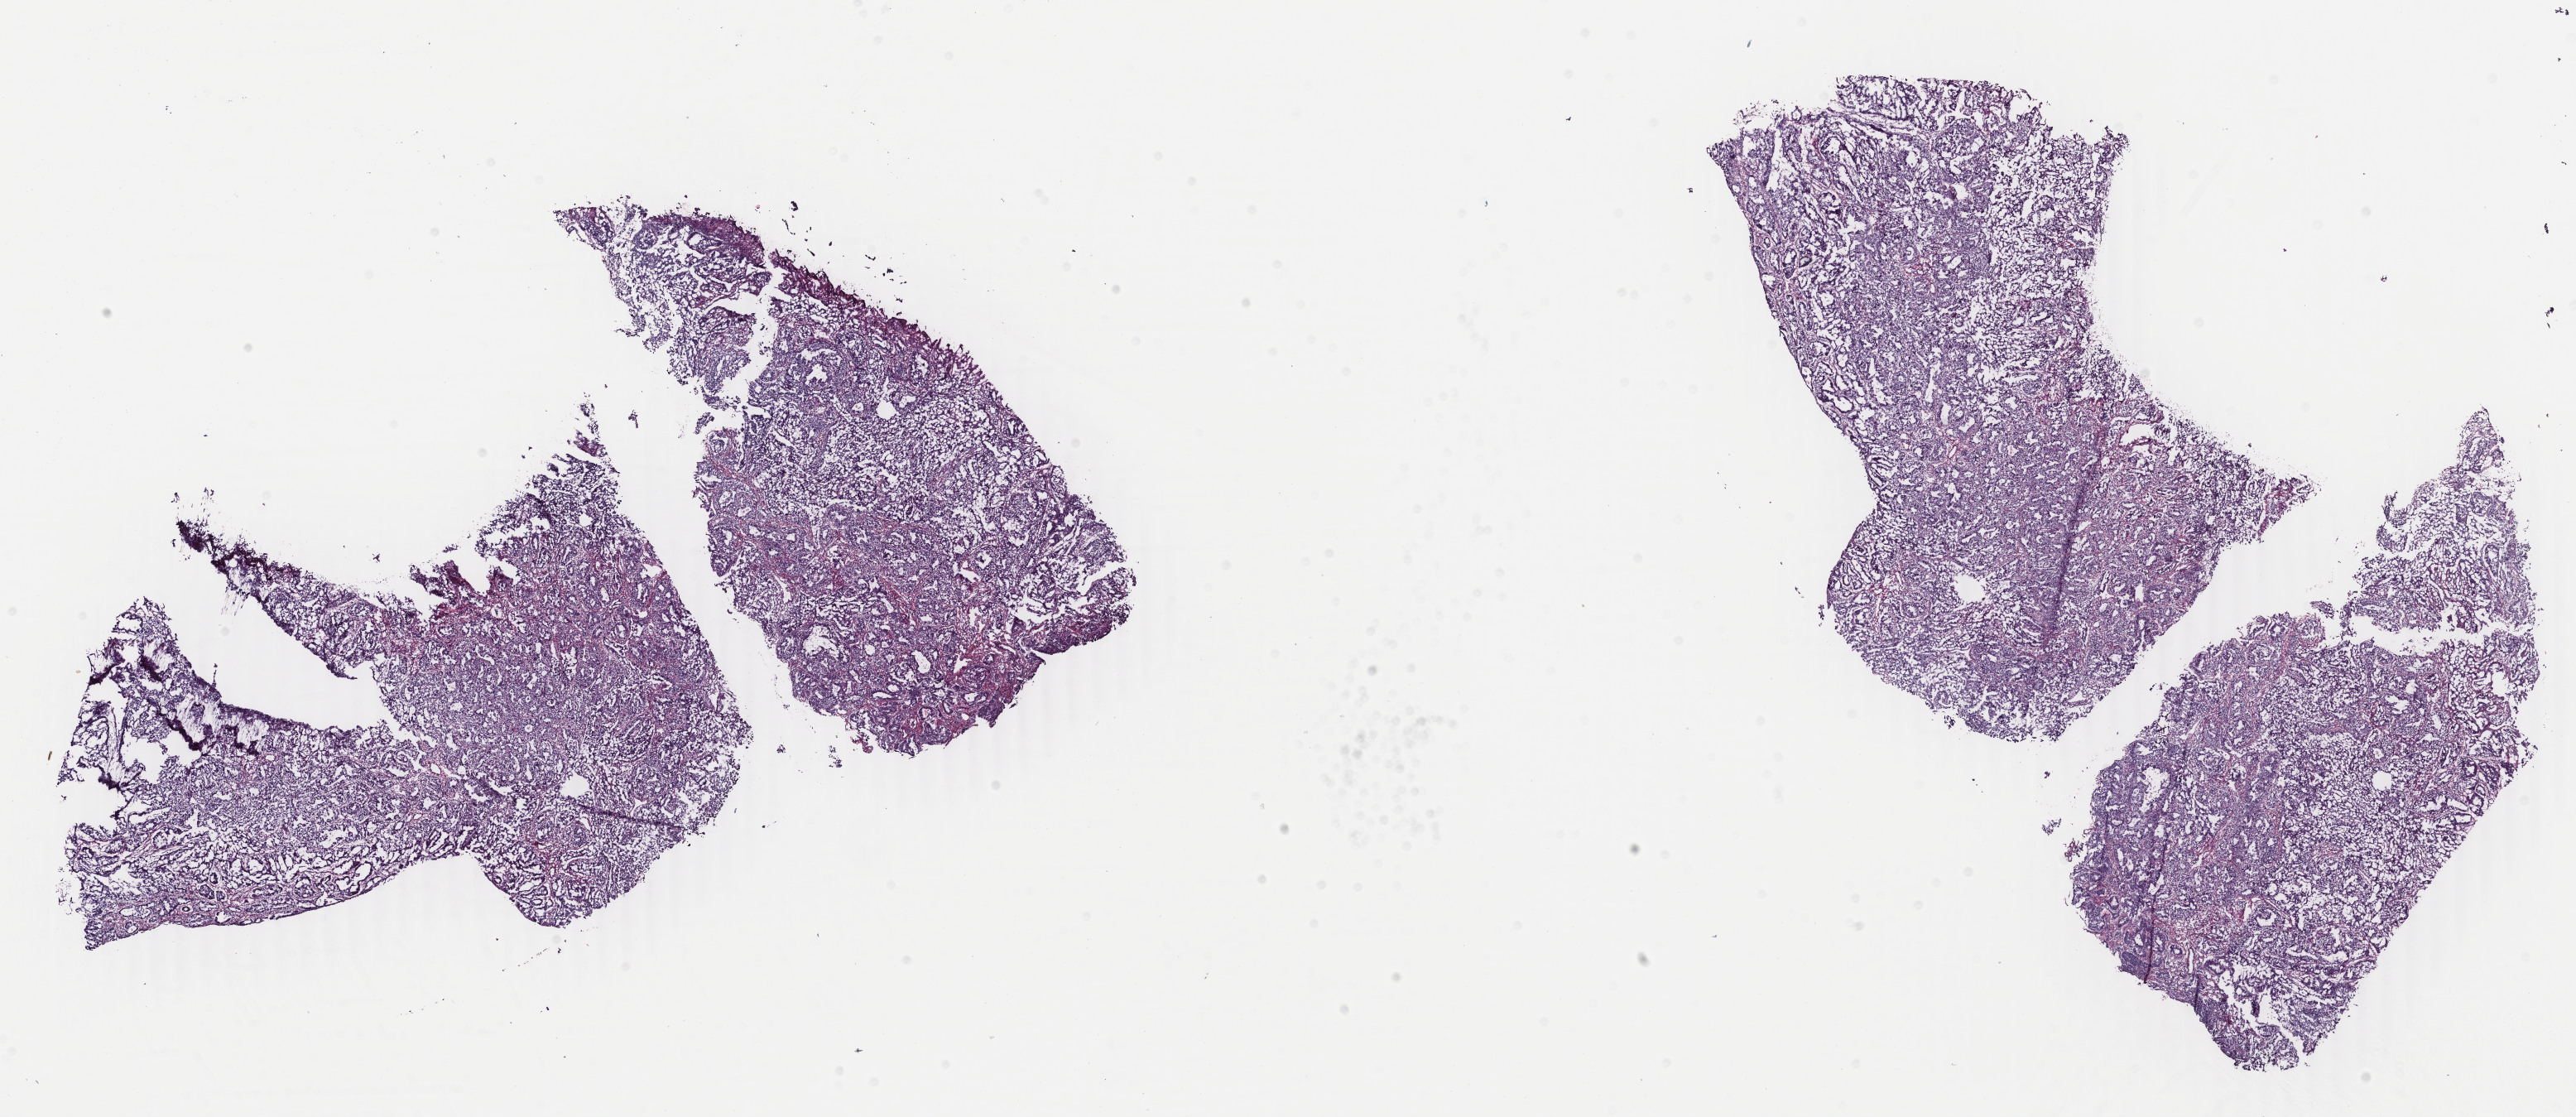
Whole-slide histology image, H&E-stained — shown as a low-resolution overview of the whole scanned area (about 24.7 x 10.7 mm, acquisition: 40x scan). Frozen section from the bottom of the tissue portion. Sample: primary tumour, uterus. Female, age 57 years at initial diagnosis. Composition of this section per pathologist review: tumour cells 70%, tumour nuclei 70%.
Diagnosis: Endometrioid adenocarcinoma, NOS.